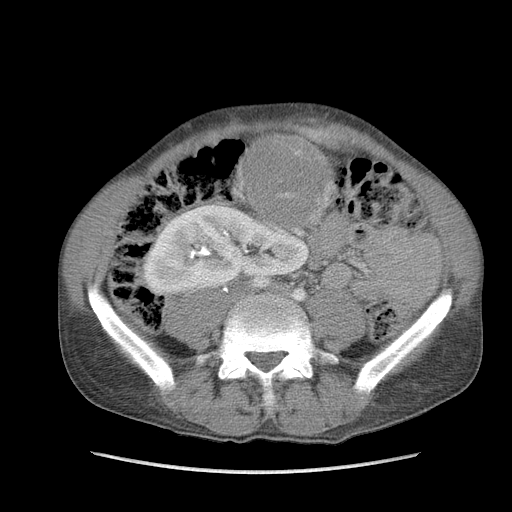
Contrast-enhanced abdominal CT, one axial slice; soft-tissue window (W 400 / L 40 HU); 512 × 512 image matrix. Male patient. From the clinical record (not read from this slice): diagnosis: adrenocortical carcinoma; tumour side: right adrenal.
Outlined on this slice (semi-automatically segmented with operator editing):
- mass: box from (x=246, y=136) to (x=328, y=225) px